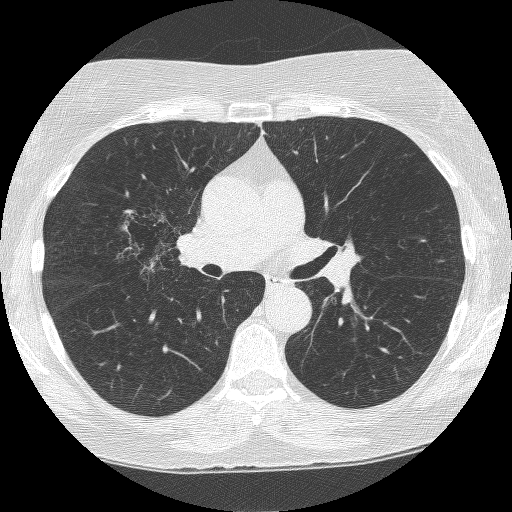
Axial slice from a low-dose chest CT screening exam; second screening round (one year after baseline); lung window (W 1500 / L -600 HU); 1.25 mm slice thickness. Female, age 64 years at enrolment. Former smoker at enrolment.
Expert reader's lesion annotation, bounding box [x1, y1, x2, y2] px = [116, 205, 201, 287]. The screening reader recorded 4 non-calcified nodules or masses ≥4 mm on this exam (right upper lobe, right upper lobe, right upper lobe, left upper lobe); which of them this box marks is not recorded.